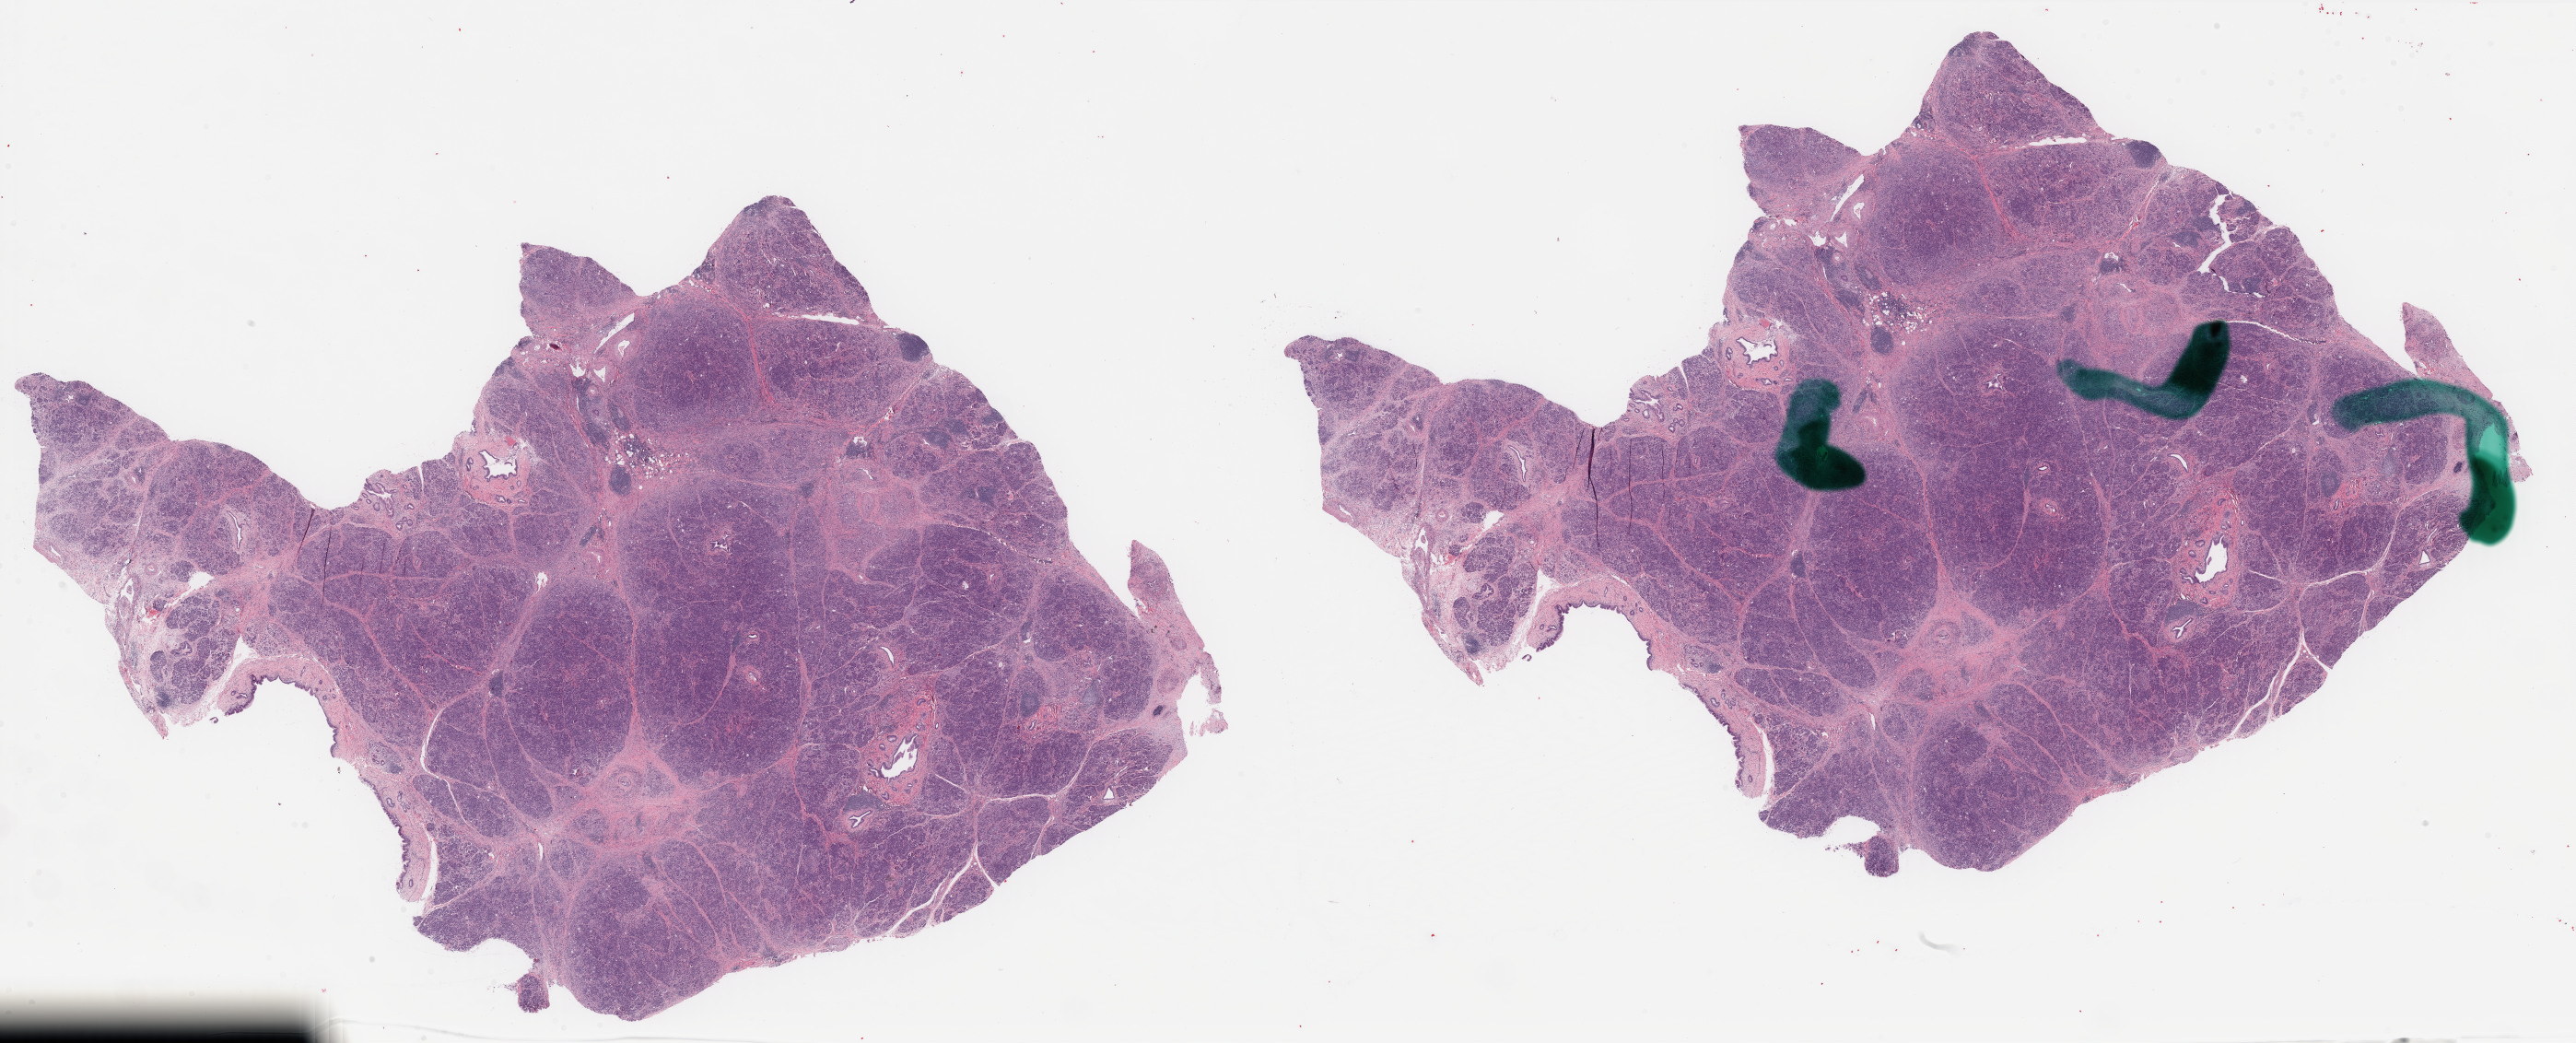
H&E-stained whole-slide image — shown as a low-resolution overview of the whole scanned area (about 44.2 x 17.9 mm, from a 40x scan). Formalin-fixed paraffin-embedded (FFPE) diagnostic section. Primary tumour sample from the pancreas. Female, age 79 years at initial diagnosis. Histologic grade: G2 (moderately differentiated).
• AJCC pathologic stage: IIB
• pathologic diagnosis: Adenocarcinoma, NOS (head of pancreas)
• TNM: T3 N1 M0